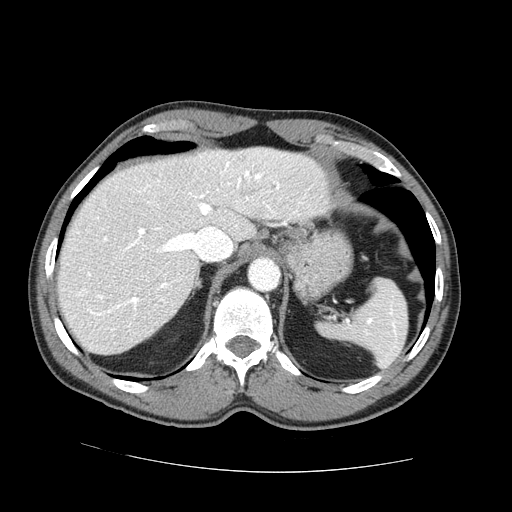
Contrast-enhanced abdominal CT (liver protocol), one axial slice; slice 55 of 73 in the series (ordered by position); reconstruction kernel STANDARD; one of 2 acquisitions stored at this slice position; soft-tissue window (W 400 / L 40 HU); 2.5 mm slice thickness; 512 × 512 image matrix. From the clinical record (not read from this slice): diagnosis: hepatocellular carcinoma (patient treated with transarterial chemoembolisation; whether this scan precedes or follows treatment is not stated here); TNM stage (as recorded): Stage-IVA; Child-Pugh class: A.
Annotated regions visible in this slice (semi-automatic segmentation, software-assisted and operator-edited):
- abdominal aorta: box from (x=249, y=257) to (x=279, y=290) px
- liver parenchyma outside the tumour (the mass and vessels are separate outlines, so this box may not span the whole liver): (x=57, y=147)–(x=329, y=354)
- liver vessels: (x=80, y=161)–(x=279, y=316)